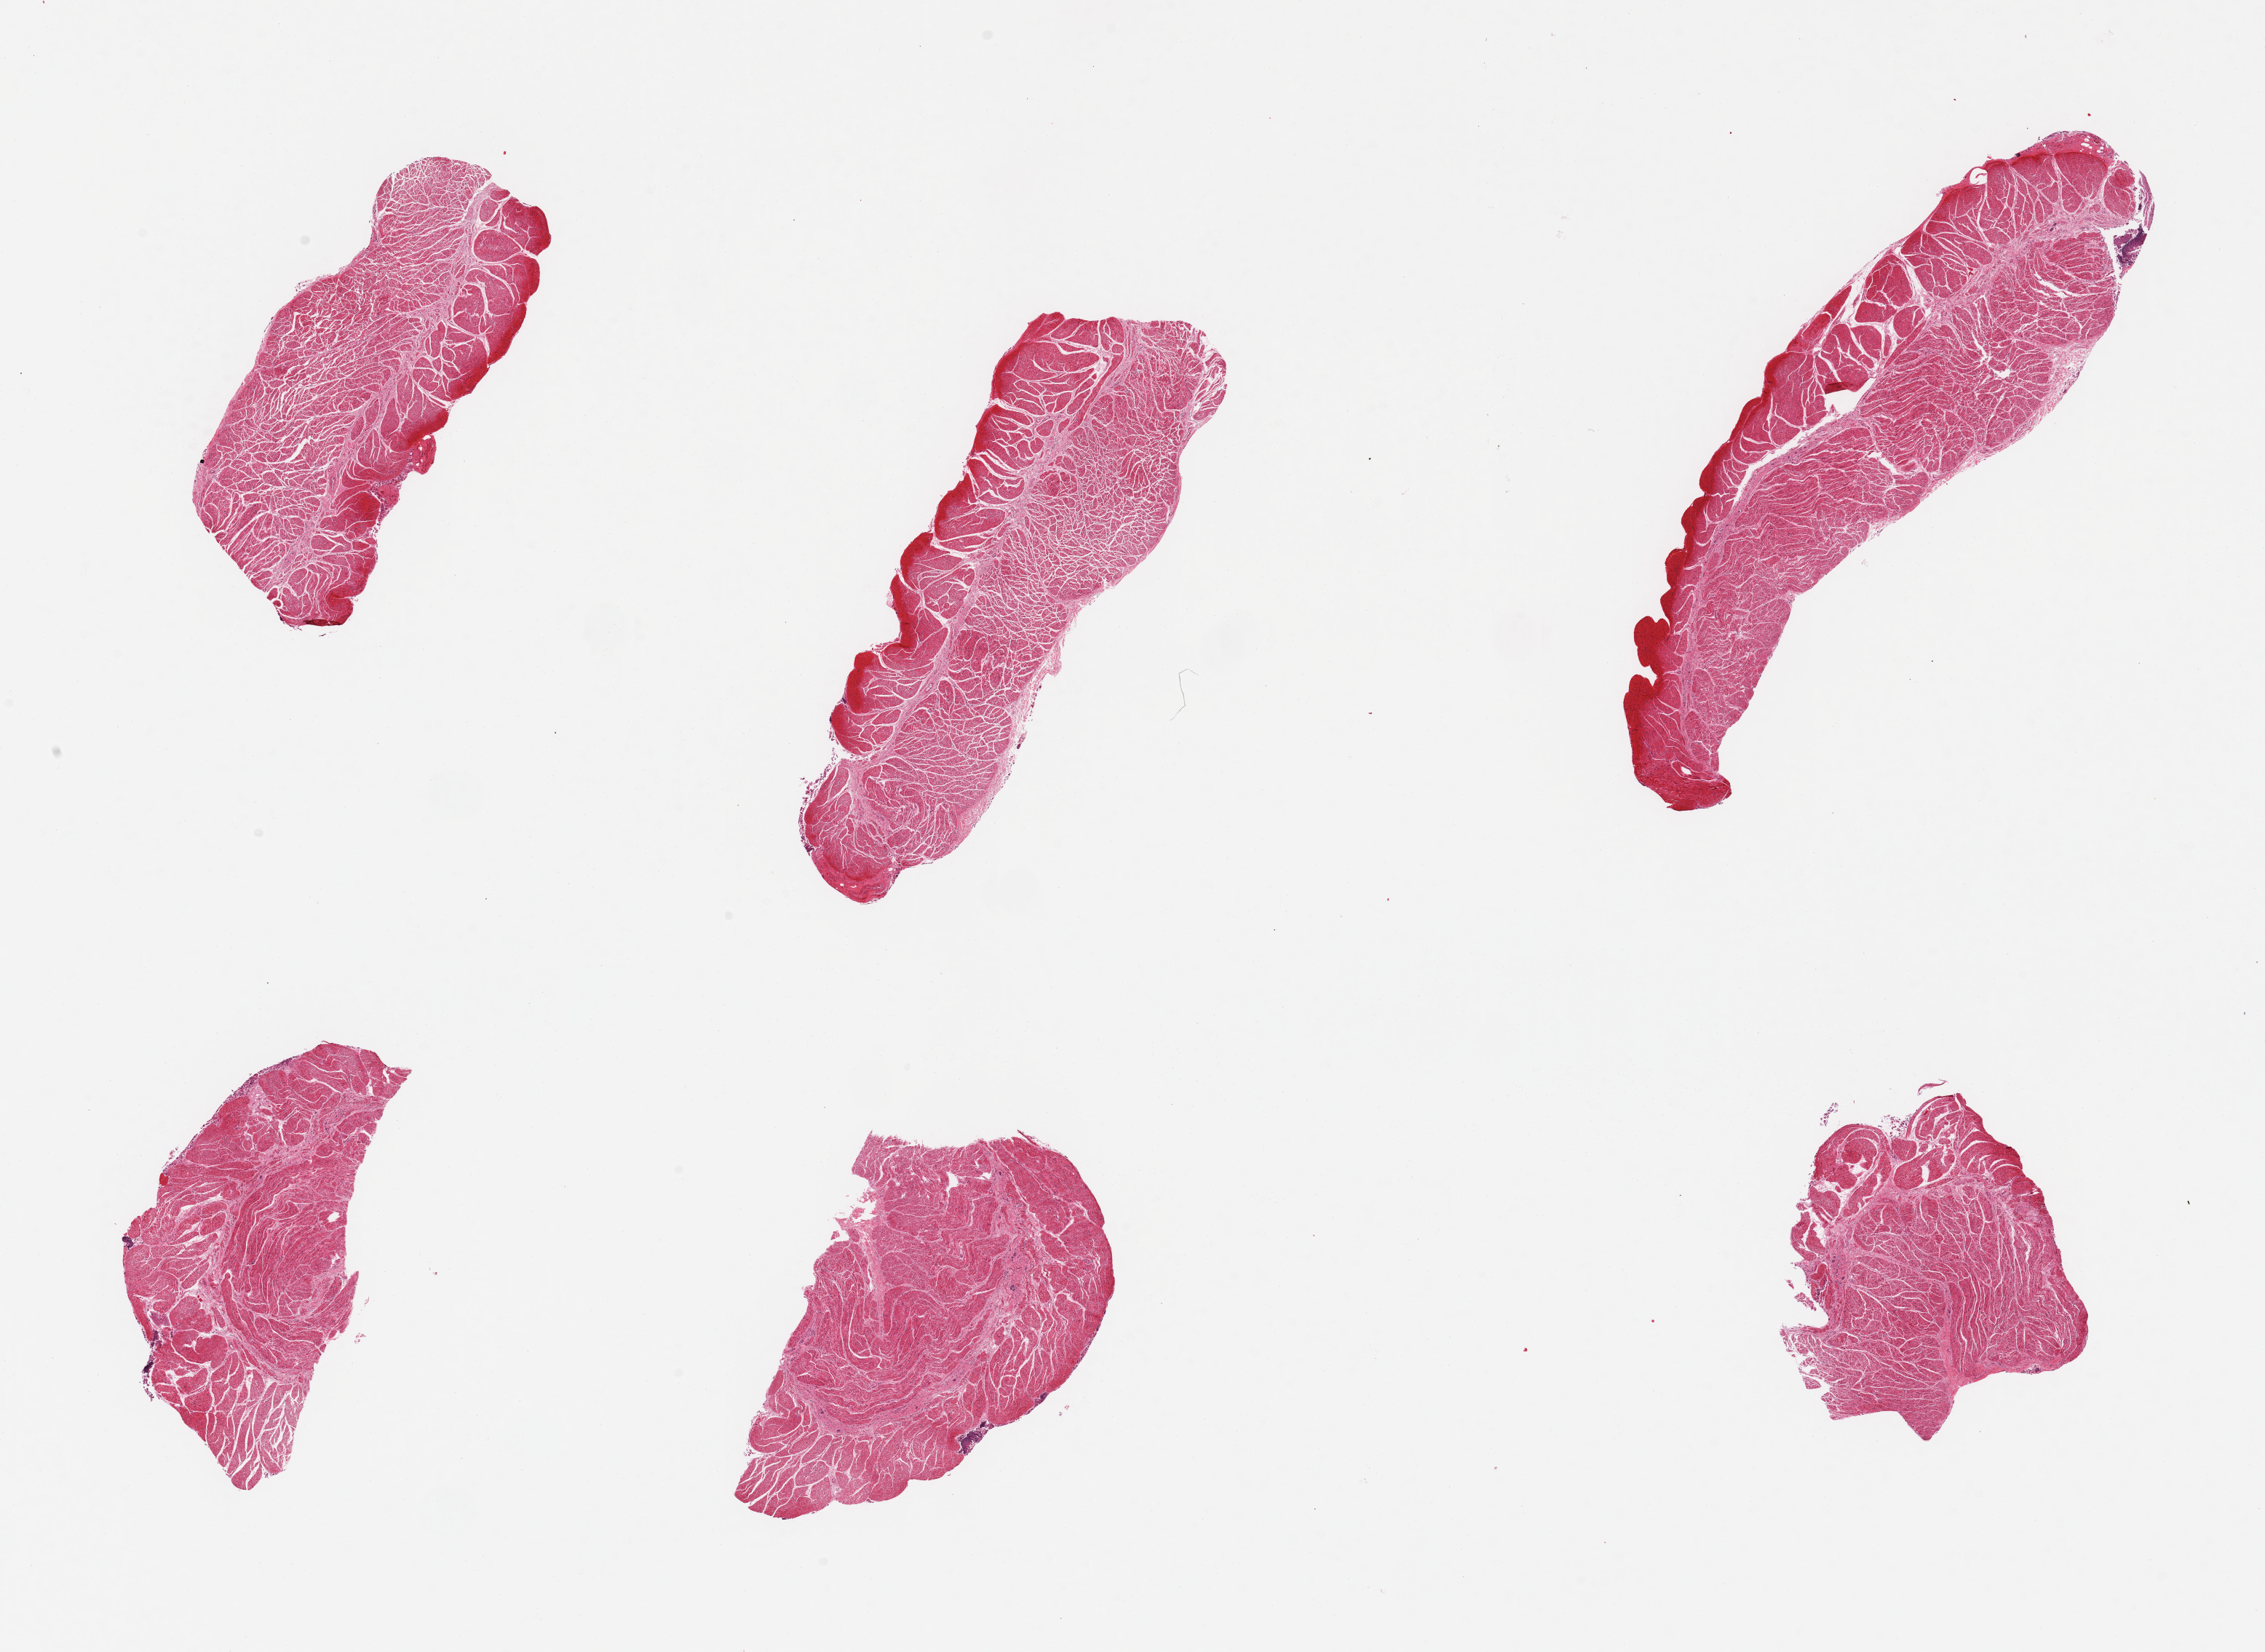
Whole-slide image, hematoxylin and eosin (H&E) stain, whole scanned area (about 24.6 x 18.0 mm, acquisition: 20x scan) shown as a low-resolution overview. PAXgene-fixed, paraffin-embedded tissue. Target tissue: esophageal muscle. Donor tissue sample. Donor: male.
Review note (as recorded): 6 pieces; half show eosinophilic edge artifact: drying, stabilizer before fixative?.